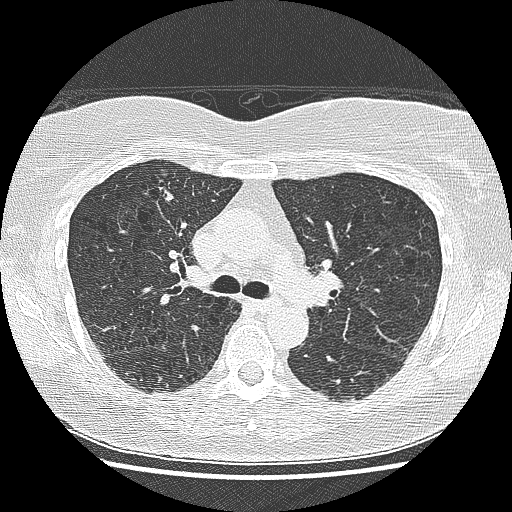
Low-dose screening chest CT, one axial slice. Slice 98 of 155 in the series (ordered by position). Reconstruction kernel LUNG. 120 kVp. Lung window (W 1500 / L -600 HU). 2.5 mm slice thickness. 512 × 512 image matrix, field of view 330 × 330 mm.
Annotated regions visible in this slice (expert manual segmentation):
- lesion 1 (tumor, upper lobe of right lung): bounding box (x1, y1, x2, y2) in pixels: (157, 184, 173, 204)